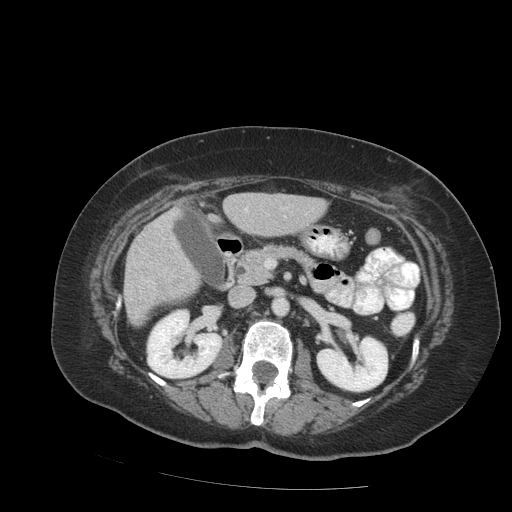
Contrast-enhanced abdominal CT (liver protocol), one axial slice. Position 35 of 99 along the scan axis. Reconstruction kernel STANDARD. 140 kVp. Soft-tissue window (W 400 / L 40 HU). 2.5 mm slice thickness. 512 × 512 image matrix. From the clinical record (not read from this slice): diagnosis: hepatocellular carcinoma (patient treated with transarterial chemoembolisation; whether this scan precedes or follows treatment is not stated here); TNM stage (as recorded): Stage-IVB; Child-Pugh class: A; tumour nodularity: uninodular.
Outlined on this slice (semi-automatic segmentation, software-assisted and operator-edited):
- liver parenchyma outside the tumour (the mass and vessels are separate outlines, so this box may not span the whole liver): box from (x=124, y=192) to (x=325, y=326) px
- liver vessels: (x=148, y=208)–(x=247, y=284)